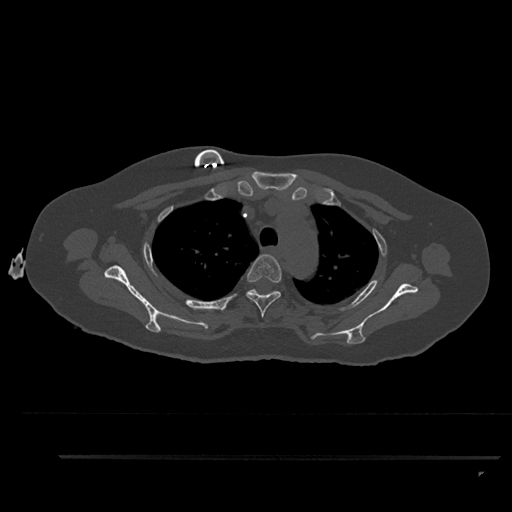
CT including the spine, one axial slice; position 677 of 797 along the scan axis; bone window (W 1800 / L 400 HU); 0.5 mm slice thickness; 512 × 512 image matrix. Patient: female, 44 years. From the clinical record (not read from this slice): primary cancer: renal; vertebrae with lytic lesions (as recorded): L1.
Outlined on this slice (semi-automatically segmented with operator editing):
- T3 vertebra: bounding box (x1, y1, x2, y2) in pixels: (246, 254, 282, 318)
- T4 vertebra: (247, 289, 275, 293)